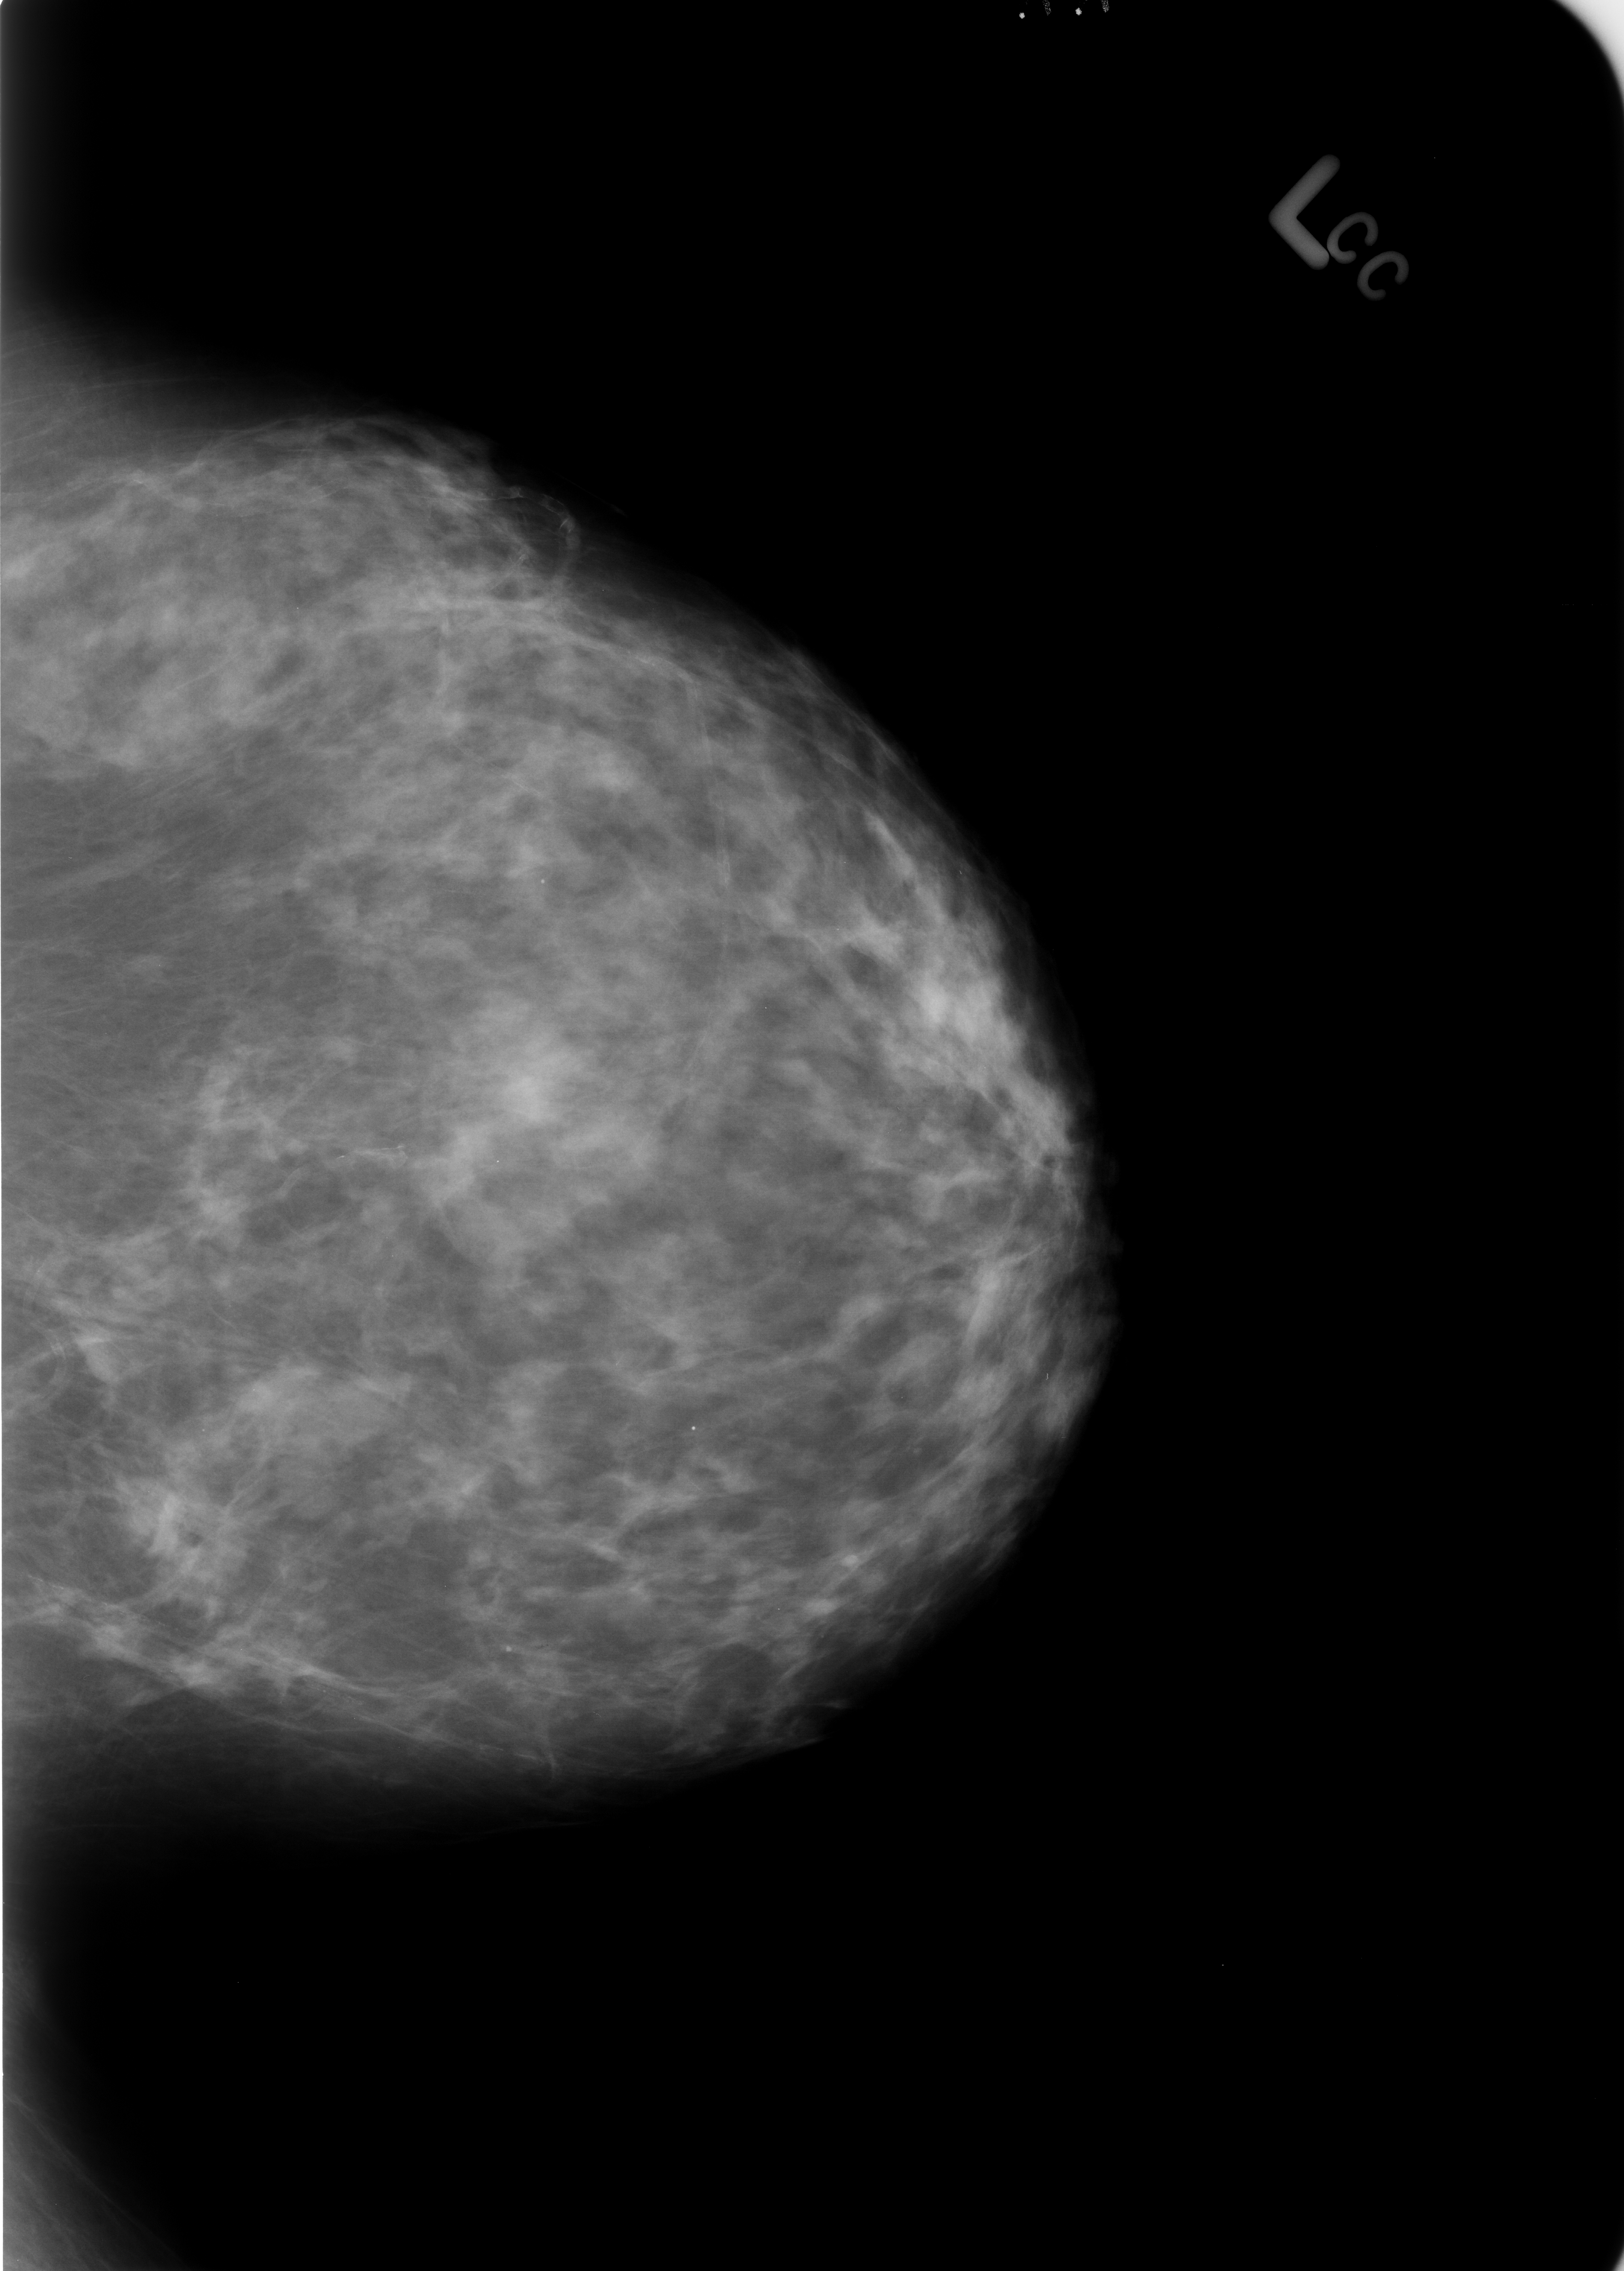
Mammogram (digitized film); left breast; CC view; breast composition: scattered fibroglandular densities (BI-RADS density category 2 of 4); 1624 × 2271 image matrix.
Expert-marked regions of interest on this film, with their recorded descriptors:
- Finding 1 of 6: calcifications, morphology vascular; BI-RADS assessment category 2; subtlety rating 4 on a 1 (subtle) to 5 (obvious) scale; outcome (as recorded, no biopsy): benign without callback (not worked up further): bounding box (x1, y1, x2, y2) in pixels: (0, 1196, 101, 1437)
- Finding 2 of 6: calcifications, morphology vascular; BI-RADS assessment category 2; outcome (as recorded, no biopsy): benign without callback (not worked up further): (0, 1578, 392, 1719)
- Finding 3 of 6: calcifications, morphology vascular; BI-RADS assessment category 2; benign; no additional work-up was recommended (outcome (as recorded, no biopsy): benign without callback): (119, 462, 476, 541)
- Finding 4 of 6: calcifications, morphology punctate; BI-RADS assessment category 2; outcome (as recorded, no biopsy): benign without callback (not worked up further): (469, 1617, 554, 1693)
- Finding 5 of 6: calcifications, morphology punctate; BI-RADS assessment category 2; benign; no additional work-up was recommended (outcome (as recorded, no biopsy): benign without callback): (501, 866, 577, 932)
- Finding 6 of 6: calcifications, morphology vascular; BI-RADS assessment category 2; benign; no additional work-up was recommended (outcome (as recorded, no biopsy): benign without callback): (504, 553, 745, 1068)